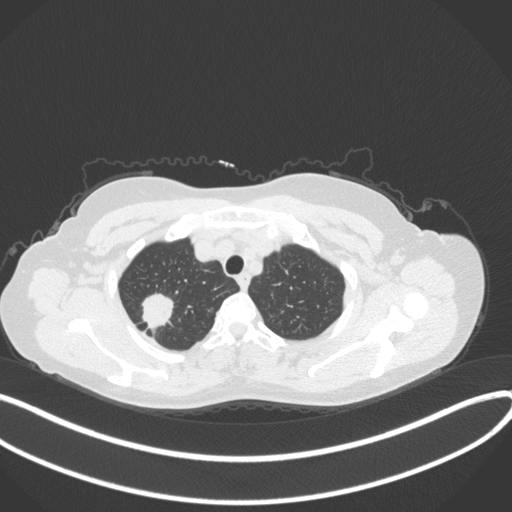
Chest CT, one axial slice. Slice 310 of 342 in the series (ordered by position). Reconstruction kernel B31f. Lung window (W 1500 / L -600 HU). 1 mm slice thickness. 512 × 512 image matrix, field of view 400 × 400 mm. Female patient, age 50 years. Case-level facts recorded for this patient, not image findings: clinical TNM (as recorded): T1c N0 M0; histopathological grade: G2-3.
Outlined on this slice (bounding box drawn by a radiologist):
- lung tumour (recorded histology: adenocarcinoma): box from (x=137, y=289) to (x=175, y=332) px